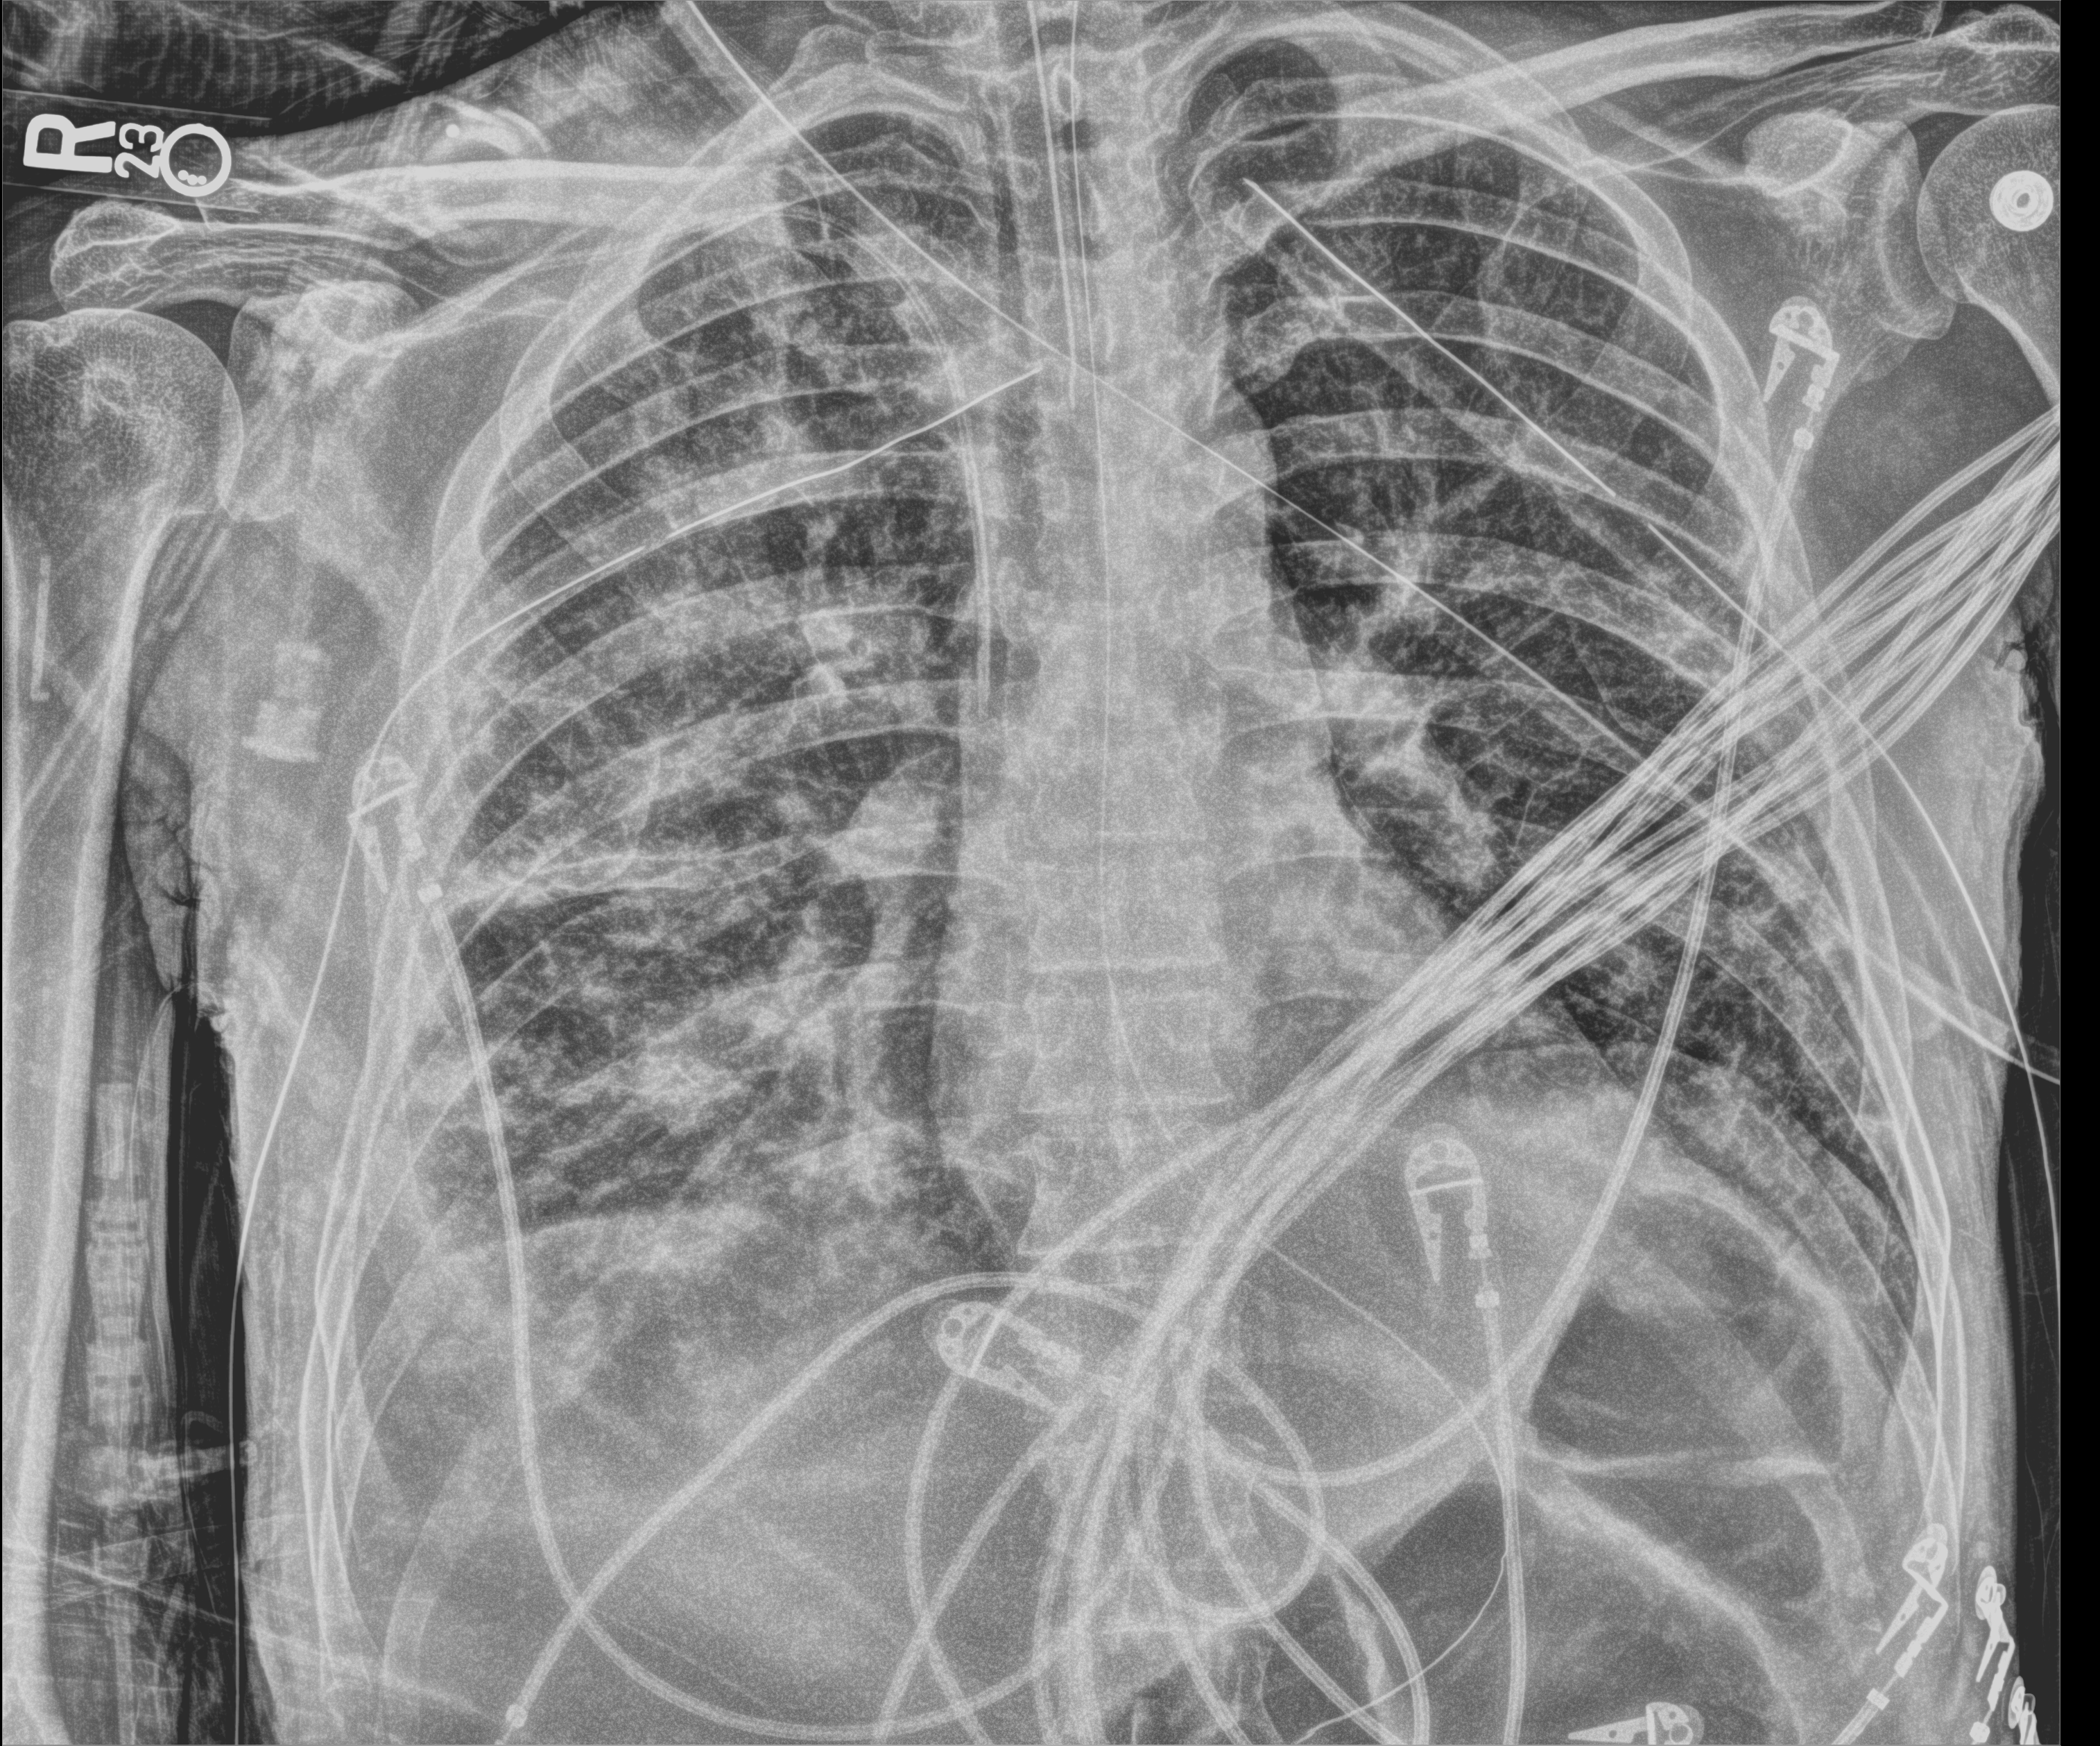
Chest X-ray (portable). Male patient hospitalised with COVID-19, age 18–59 years.
Admission-level facts for this patient (not findings on this image; timing relative to this image not recorded): mechanically ventilated during this hospital stay: yes; admitted to intensive care during this hospital stay: yes; other chronic lung disease (admission record): no.